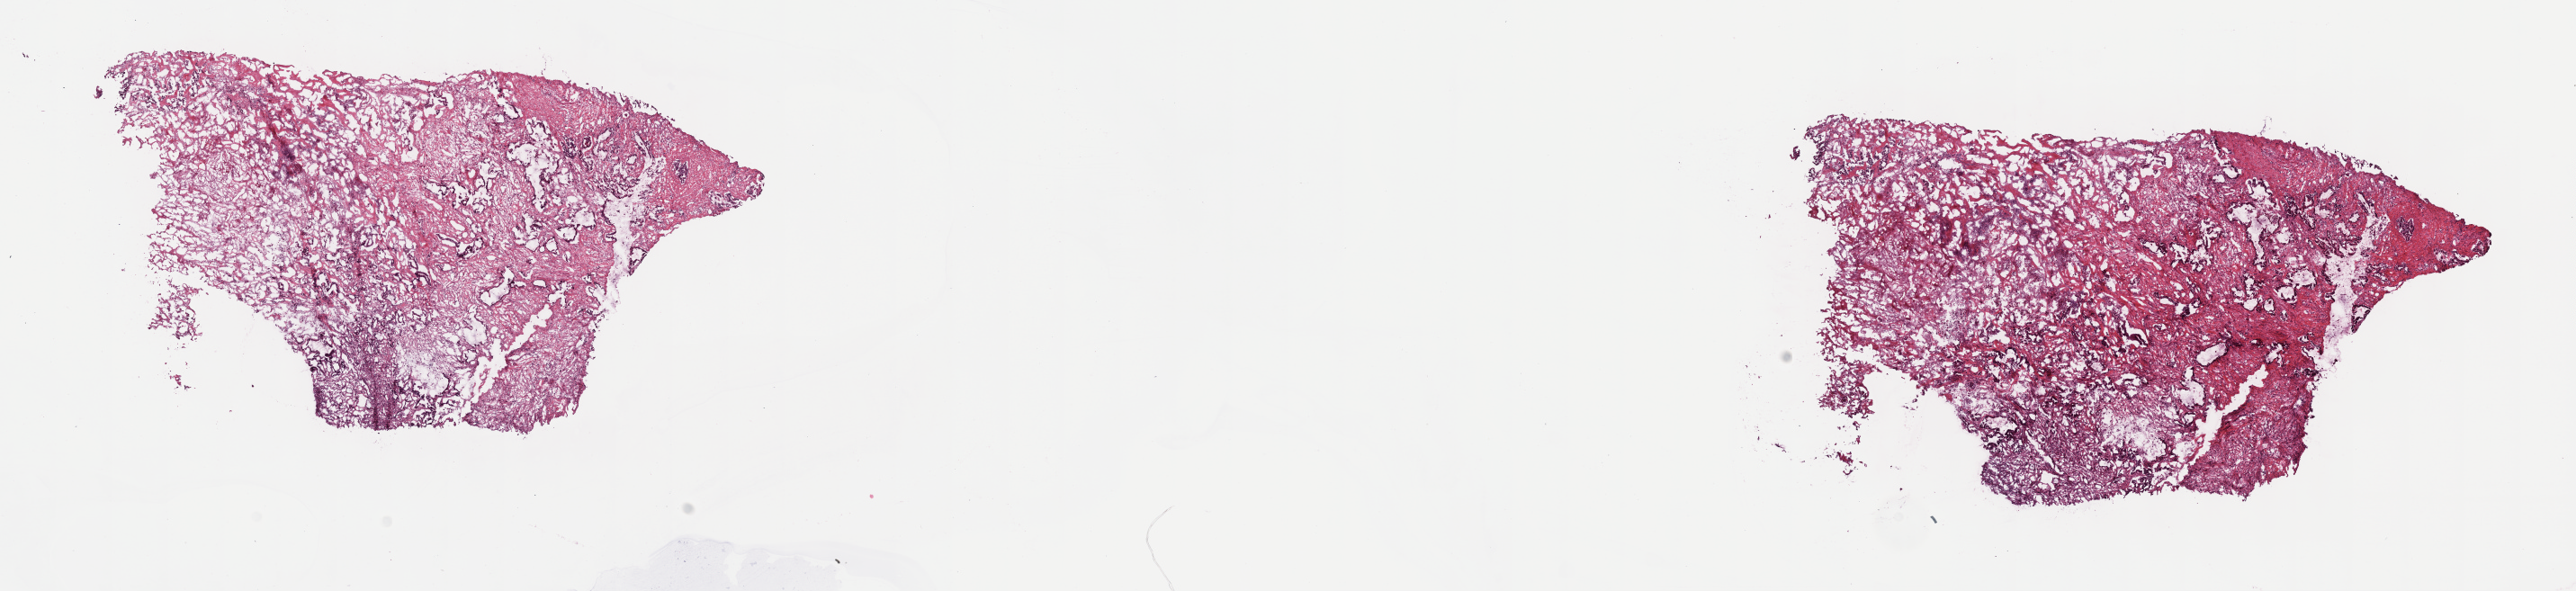
Digitized H&E-stained tissue section (whole slide), a low-resolution overview of the entire scanned area, about 23.2 x 5.3 mm, frozen section from the top of the tissue portion, bile duct, primary tumour sample. Male patient; age at initial diagnosis 75 years.
Pathologic diagnosis: Cholangiocarcinoma (intrahepatic bile duct).